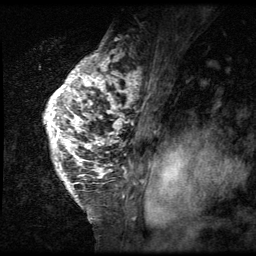
Breast MRI (dynamic contrast-enhanced), one sagittal slice. Position 46 of 64 along the scan axis. 3 images stored at this slice position (order not interpretable as contrast timing). 1.5 T. TE 4.2 ms, TR 9 ms. 256 × 256 image matrix, field of view 180 × 180 mm. Patient: female, 50 years. Case-level facts recorded for this patient, not image findings: setting: breast cancer imaged before/during neoadjuvant chemotherapy; receptor status: triple-negative.
Structures marked on this image (semi-automatically segmented with operator editing):
- analysis volume of interest (the breast-tissue region the enhancement analysis was run in; not a lesion): bounding box <38,39,139,212> (left, top, right, bottom; pixels)
- tumour enhancement mask (voxels above the 140 % enhancement threshold inside the analysis volume of interest): <43,52,139,198>